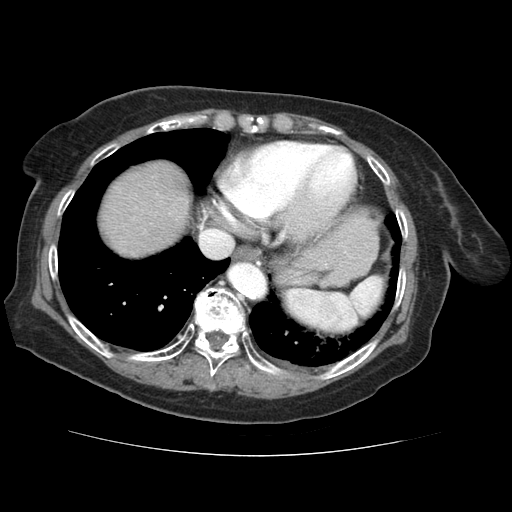
Contrast-enhanced abdominal CT (liver protocol), one axial slice; 120 kVp; soft-tissue window (W 400 / L 40 HU); 2.5 mm slice thickness; 512 × 512 image matrix, field of view 360 × 360 mm. From the clinical record (not read from this slice): diagnosis: hepatocellular carcinoma (patient treated with transarterial chemoembolisation; whether this scan precedes or follows treatment is not stated here); TNM stage (as recorded): Stage-IVB; Child-Pugh class: A.
Structures marked on this image (semi-automatic segmentation, software-assisted and operator-edited):
- liver parenchyma outside the tumour (the mass and vessels are separate outlines, so this box may not span the whole liver): bounding box [x1, y1, x2, y2] px = [100, 162, 190, 256]